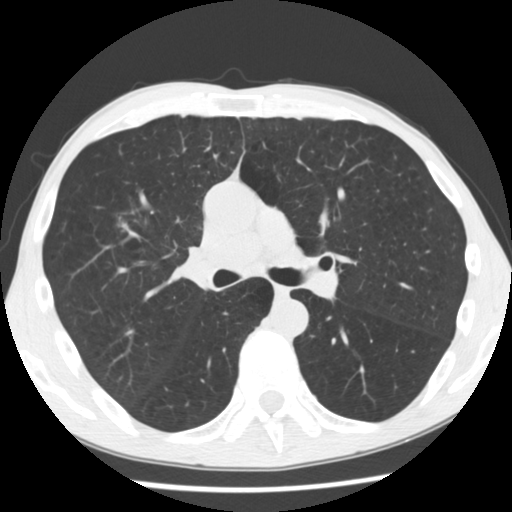
Low-dose screening chest CT, axial slice, baseline annual screen, lung window (W 1500 / L -600 HU), 2.5 mm slice thickness, standard (soft-tissue) reconstruction kernel (STANDARD), slice 123 of 292 in the series. Male, age 56 years at enrolment. Current smoker at enrolment.
Expert reader's lesion annotation, bounding box <100,205,149,248> (left, top, right, bottom; pixels). The screening reader recorded 2 non-calcified nodules or masses ≥4 mm on this exam (right upper lobe, right upper lobe); which of them this box marks is not recorded. Official screen result: positive, change unspecified: nodule(s) >= 4 mm or enlarging nodule(s), mass(es), or other non-specific abnormalities suspicious for lung cancer.